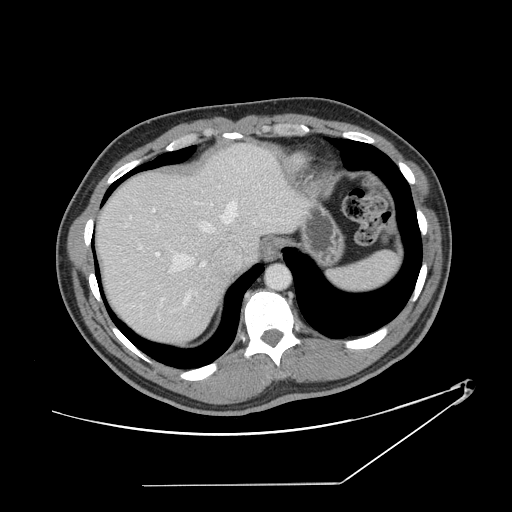
Contrast-enhanced abdominal CT, one axial slice; position 120 of 152 along the scan axis; reconstruction kernel STANDARD; 120 kVp; intravenous contrast given; soft-tissue window (W 400 / L 40 HU); 2.5 mm slice thickness; 512 × 512 image matrix. Male patient, age 45 years. From the clinical record (not read from this slice): diagnosis: colorectal cancer liver metastases, imaged before liver resection; multiple liver metastases: no; largest metastasis: 1 cm; disease in both lobes: no.
Annotated regions visible in this slice (manually delineated by an expert):
- hepatic veins: bounding box (x1, y1, x2, y2) in pixels: (111, 200, 239, 307)
- liver: (98, 147, 303, 343)
- planned liver remnant (the part of the liver to remain after resection): (99, 171, 234, 344)
- portal vein (with intrahepatic branches): (155, 252, 192, 311)